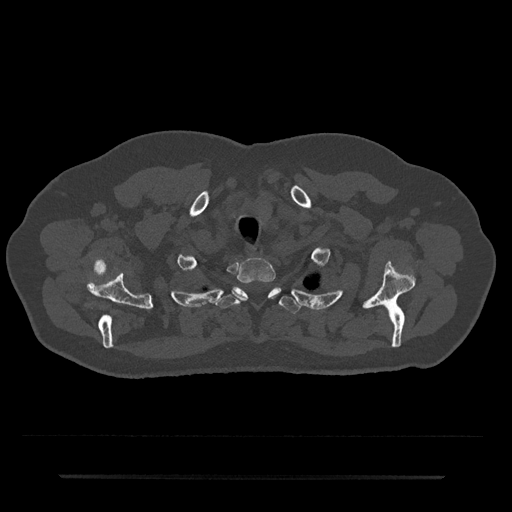
CT including the spine, one axial slice; slice 622 of 797 in the series (ordered by position); 120 kVp; bone window (W 1800 / L 400 HU); 0.5 mm slice thickness; 512 × 512 image matrix, field of view 437 × 437 mm. Male patient, age 69 years. Case-level facts recorded for this patient, not image findings: primary cancer: prostate.
Structures marked on this image (semi-automatic segmentation, software-assisted and operator-edited):
- T1 vertebra: box from (x=237, y=258) to (x=276, y=299) px
- T2 vertebra: (x=217, y=287)–(x=300, y=313)